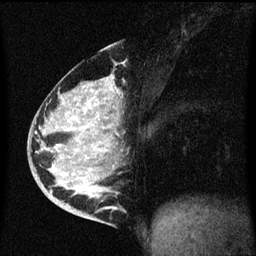
Breast MRI (dynamic contrast-enhanced), one sagittal slice; position 29 of 60 along the scan axis; dynamic contrast-enhanced series, image 2 of 3 at this slice position (ordered by acquisition); 1.5 T; TE 4.2 ms, TR 8.4 ms; 256 × 256 image matrix. Patient: female, 34 years. Case-level facts recorded for this patient, not image findings: setting: breast cancer imaged before/during neoadjuvant chemotherapy; receptor status: HR-positive, HER2-negative.
Annotated regions visible in this slice (semi-automatically segmented with operator editing):
- analysis volume of interest (the breast-tissue region the enhancement analysis was run in; not a lesion): bounding box (x1, y1, x2, y2) in pixels: (34, 48, 123, 215)
- tumour enhancement mask (voxels above the 70 % enhancement threshold inside the analysis volume of interest): (54, 84, 113, 193)